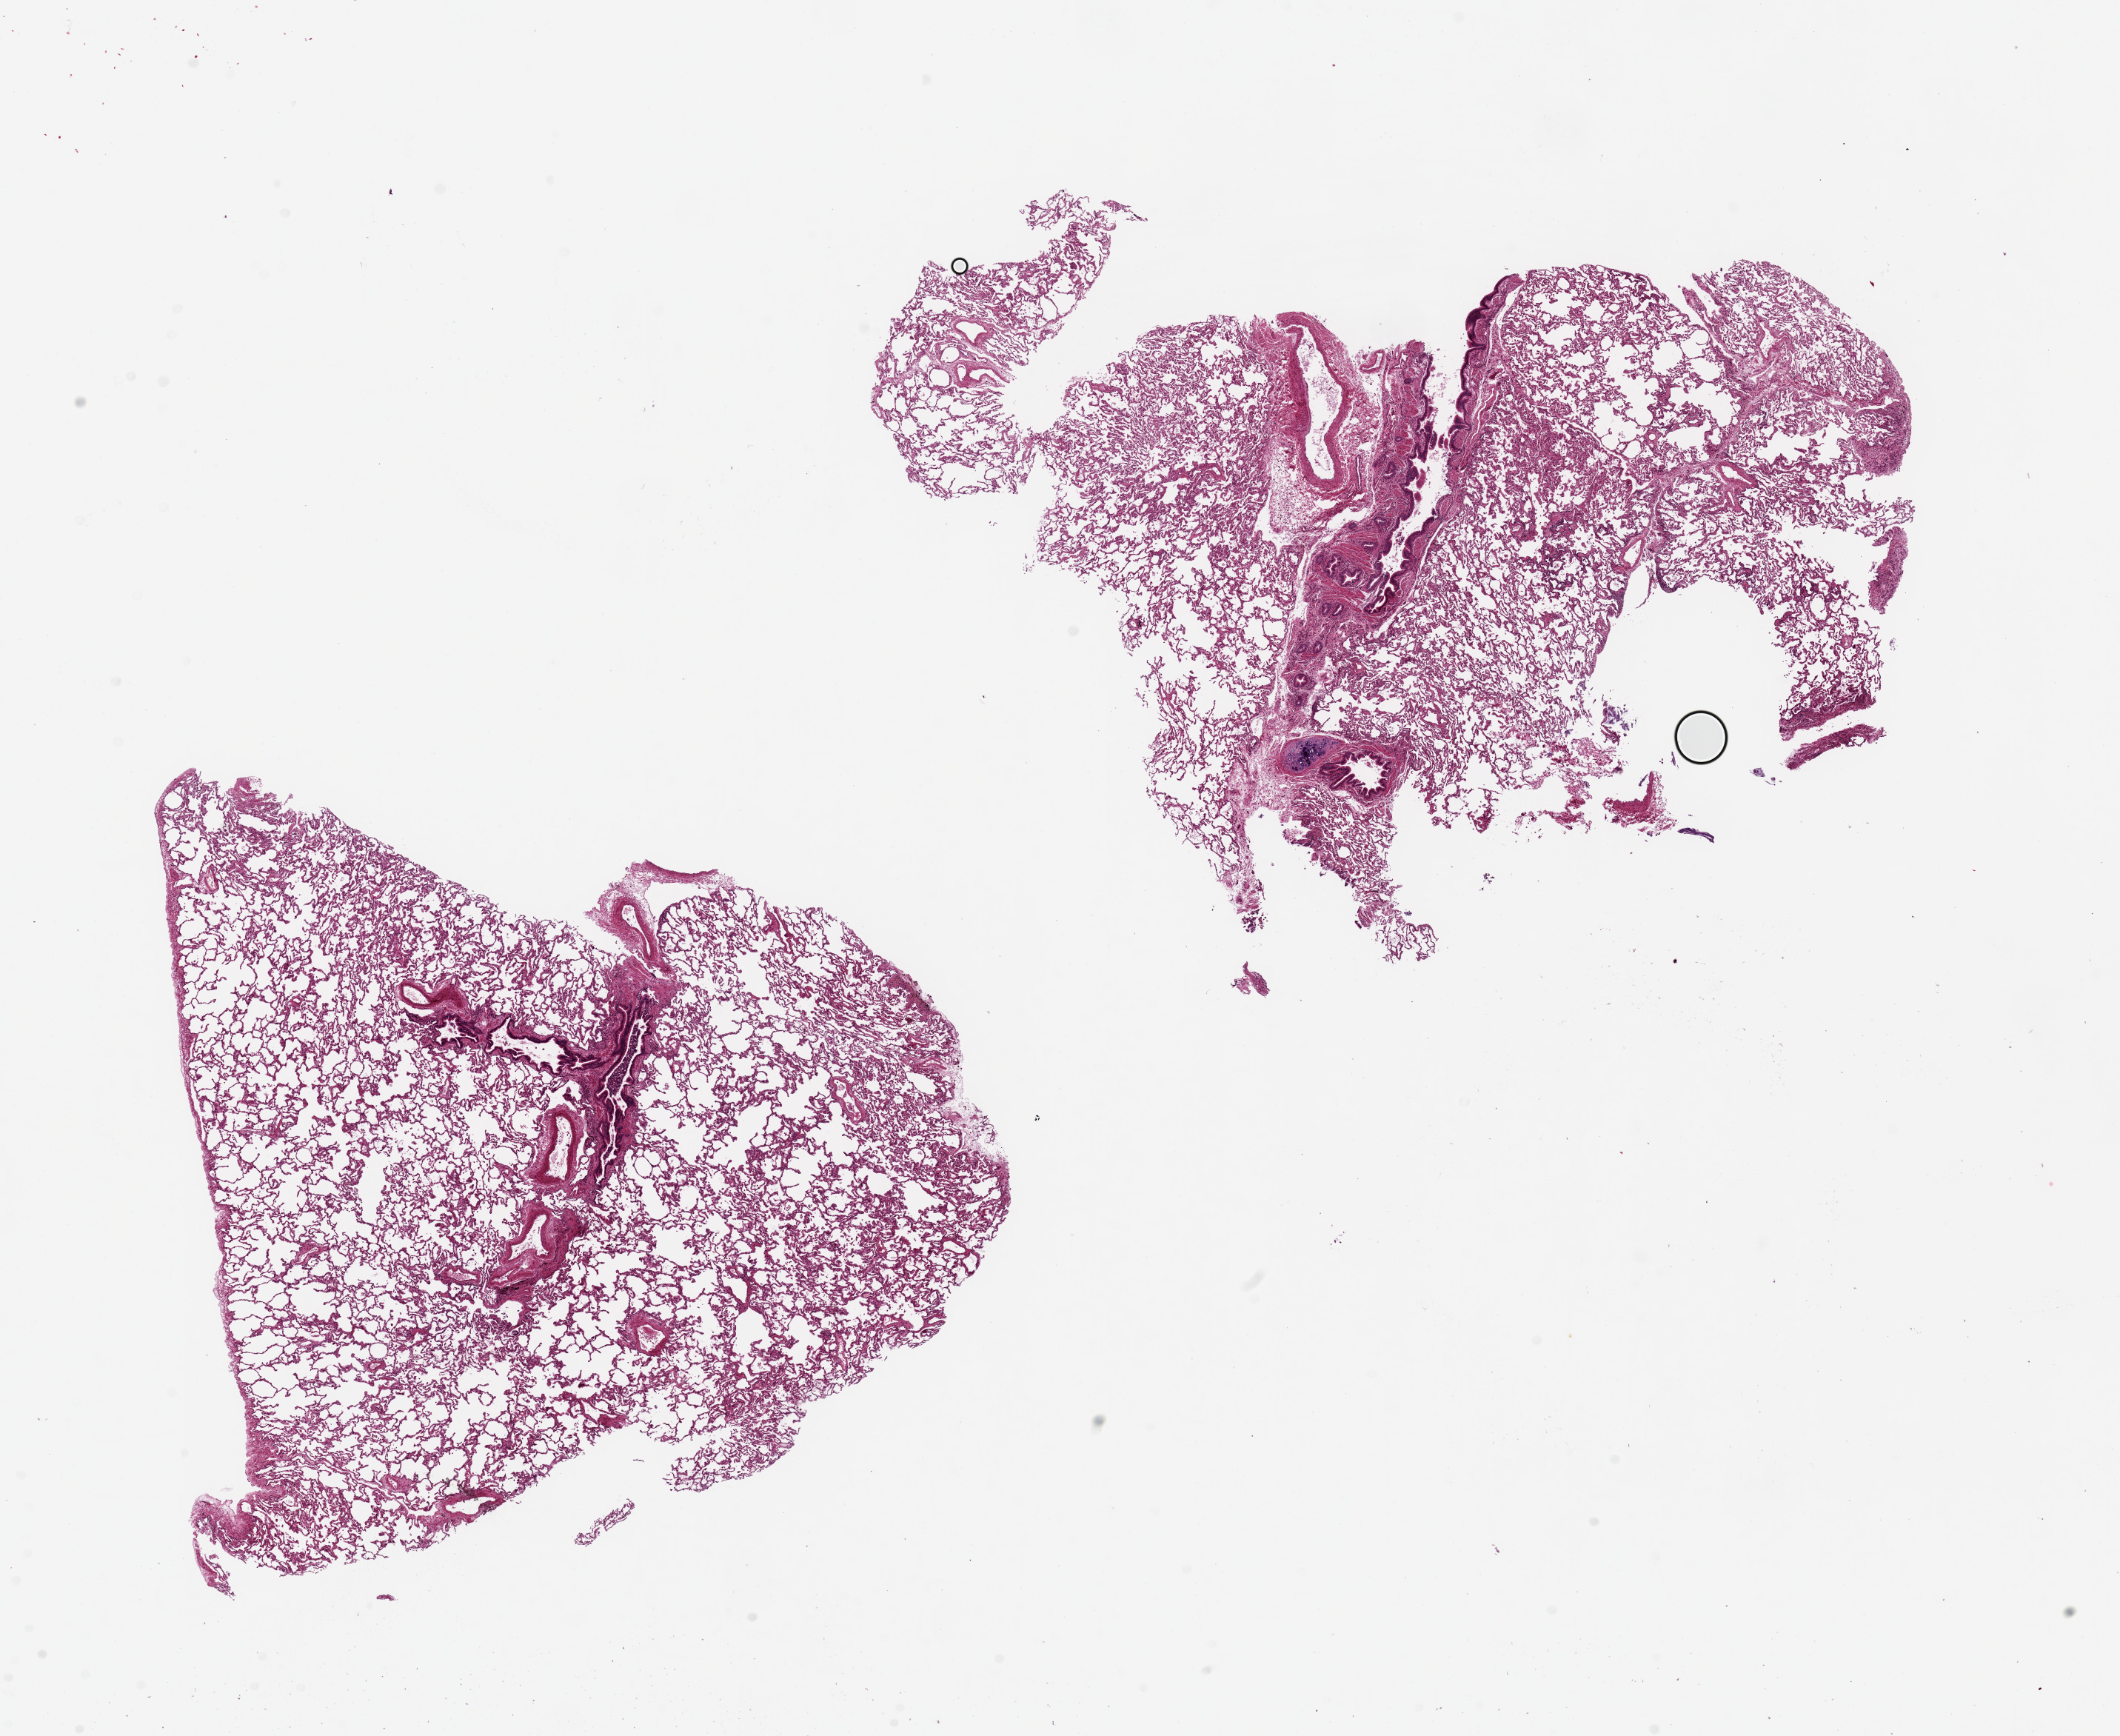
Haematoxylin and eosin whole-slide image, brightfield, shown as a low-resolution overview of the whole scanned area (about 22.6 x 18.5 mm); PAXgene-fixed paraffin-embedded (PFPE) section; sampled site (target tissue): lung; tissue donor sample. Male donor.
Reviewer comment on this tissue sample: 2 pieces ~1x7mm; Abundant vessels, bronchial/bronchiolar epithelial elements present.